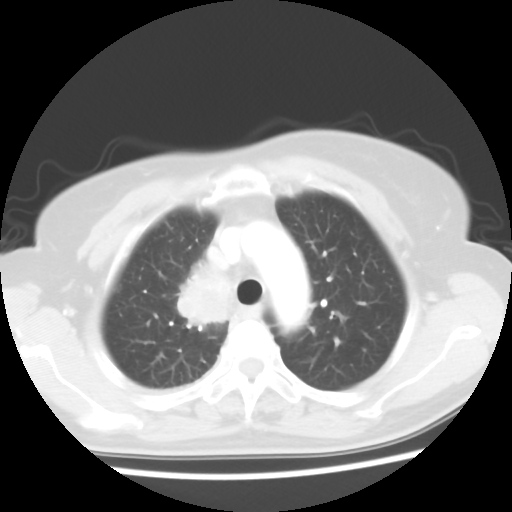
Chest CT, one axial slice. Slice 44 of 56 in the series (ordered by position). Reconstruction kernel STANDARD. 120 kVp. Lung window (W 1500 / L -600 HU). 5 mm slice thickness. 512 × 512 image matrix, field of view 314 × 314 mm. Female patient, age 62 years. Case-level facts recorded for this patient, not image findings: clinical TNM (as recorded): T2 N1 M1a.
Structures marked on this image (bounding box drawn by a radiologist):
- lung tumour (recorded histology: adenocarcinoma): bounding box (x1, y1, x2, y2) in pixels: (171, 245, 226, 334)